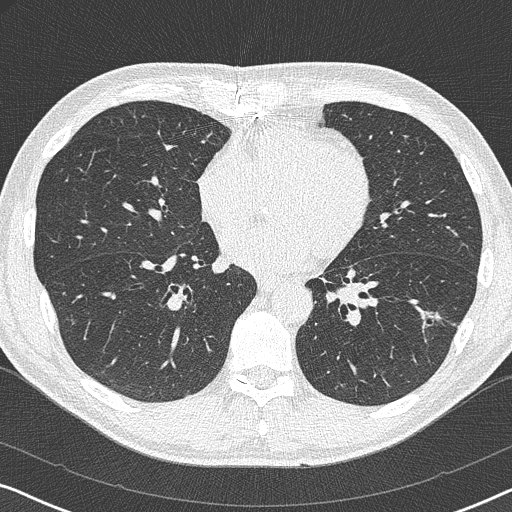
Low-dose screening chest CT, axial slice; first (baseline) screen; lung window (W 1500 / L -600 HU). Male participant, aged 59 years at enrolment. Current smoker at enrolment.
- Lesion marked by an expert reader, bounding box [x1, y1, x2, y2] px = [417, 300, 453, 344].
- The screening reader recorded 2 non-calcified nodules or masses ≥4 mm on this exam (left lower lobe, right middle lobe); which of them this box marks is not recorded.
- Official screen result: positive, change unspecified: nodule(s) >= 4 mm or enlarging nodule(s), mass(es), or other non-specific abnormalities suspicious for lung cancer.